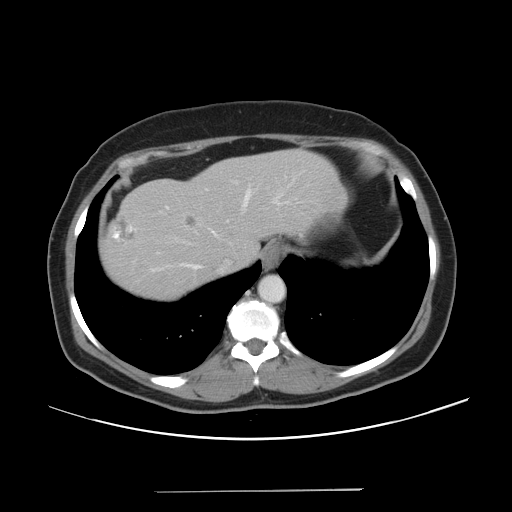
Contrast-enhanced abdominal CT, one axial slice. Position 39 of 56 along the scan axis. 120 kVp. Intravenous contrast given. Soft-tissue window (W 400 / L 40 HU). 5 mm slice thickness. 512 × 512 image matrix. Female patient, age 54 years. Case-level facts recorded for this patient, not image findings: diagnosis: colorectal cancer liver metastases, imaged before liver resection; multiple liver metastases: yes; largest metastasis: 3.2 cm.
Outlined on this slice (expert manual segmentation):
- hepatic veins: bounding box (x1, y1, x2, y2) in pixels: (149, 187, 288, 272)
- liver: (103, 150, 343, 301)
- planned liver remnant (the part of the liver to remain after resection): (199, 150, 342, 270)
- liver metastasis: (112, 216, 134, 241)
- liver metastasis: (186, 216, 196, 228)